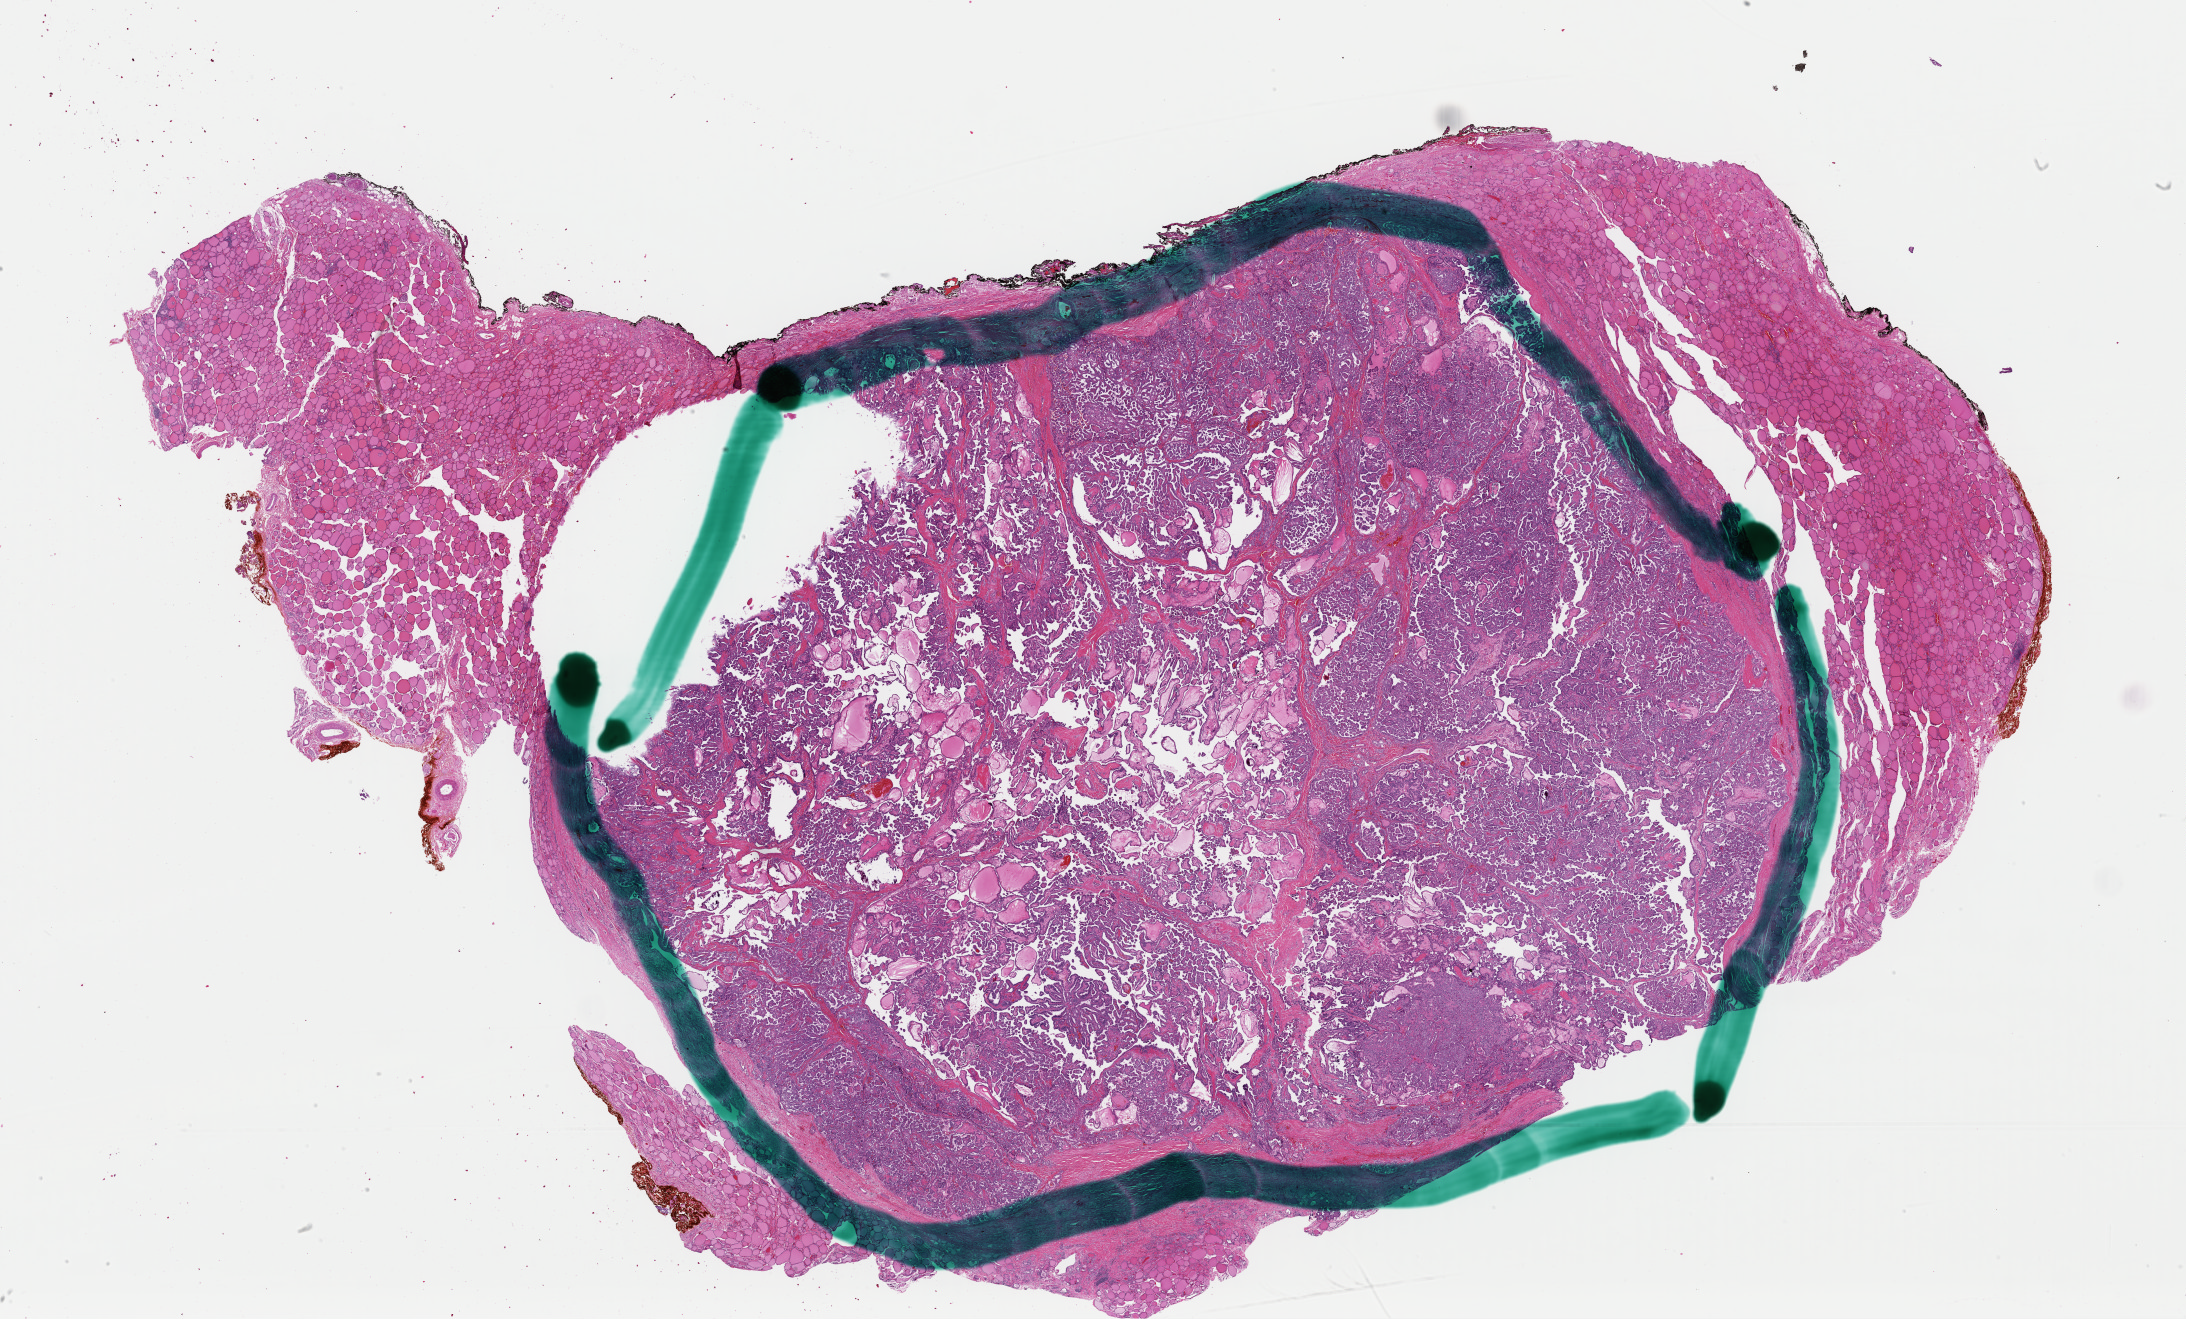
Digitized Hematoxylin and eosin (H&E) stained tissue section (whole slide) — whole scanned area (about 34.5 x 20.8 mm, from a 40x scan) shown as a low-resolution overview. FFPE section. Thyroid, primary tumour sample. Female patient; age at initial diagnosis 50 years.
- AJCC pathologic stage: III (6th edition)
- pathologic diagnosis: Papillary adenocarcinoma, NOS (thyroid gland)
- lymph nodes positive (case pathology): 2 of 8 examined